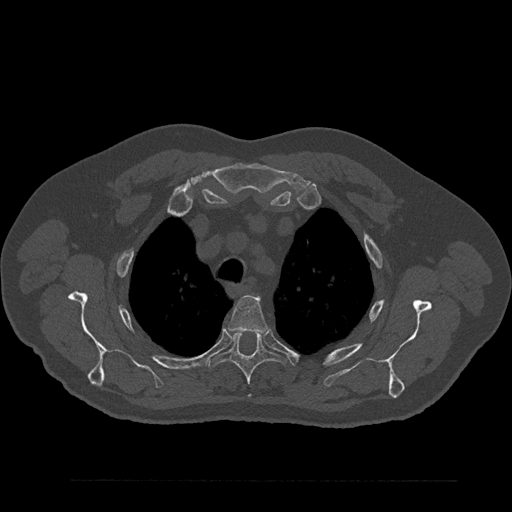
CT including the spine, one axial slice; position 657 of 797 along the scan axis; 120 kVp; bone window (W 1800 / L 400 HU); 0.5 mm slice thickness; 512 × 512 image matrix, field of view 430 × 430 mm. Patient: male, 61 years. From the clinical record (not read from this slice): primary cancer: prostate.
Outlined on this slice (semi-automatically segmented with operator editing):
- T3 vertebra: bounding box <228,295,267,333> (left, top, right, bottom; pixels)
- T4 vertebra: <207,330,286,399>